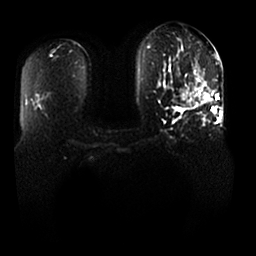
Breast MRI, one axial slice; slice 11 of 25 in the series (ordered by position); diffusion-weighted series; image 2 of 4 stored at this slice position (different b-values; order by instance number); 1.5 T; 4 mm slice thickness; 256 × 256 image matrix. Female patient.
Annotated regions visible in this slice (manually delineated by an expert):
- tumour on diffusion-weighted imaging: box from (x=173, y=82) to (x=206, y=107) px